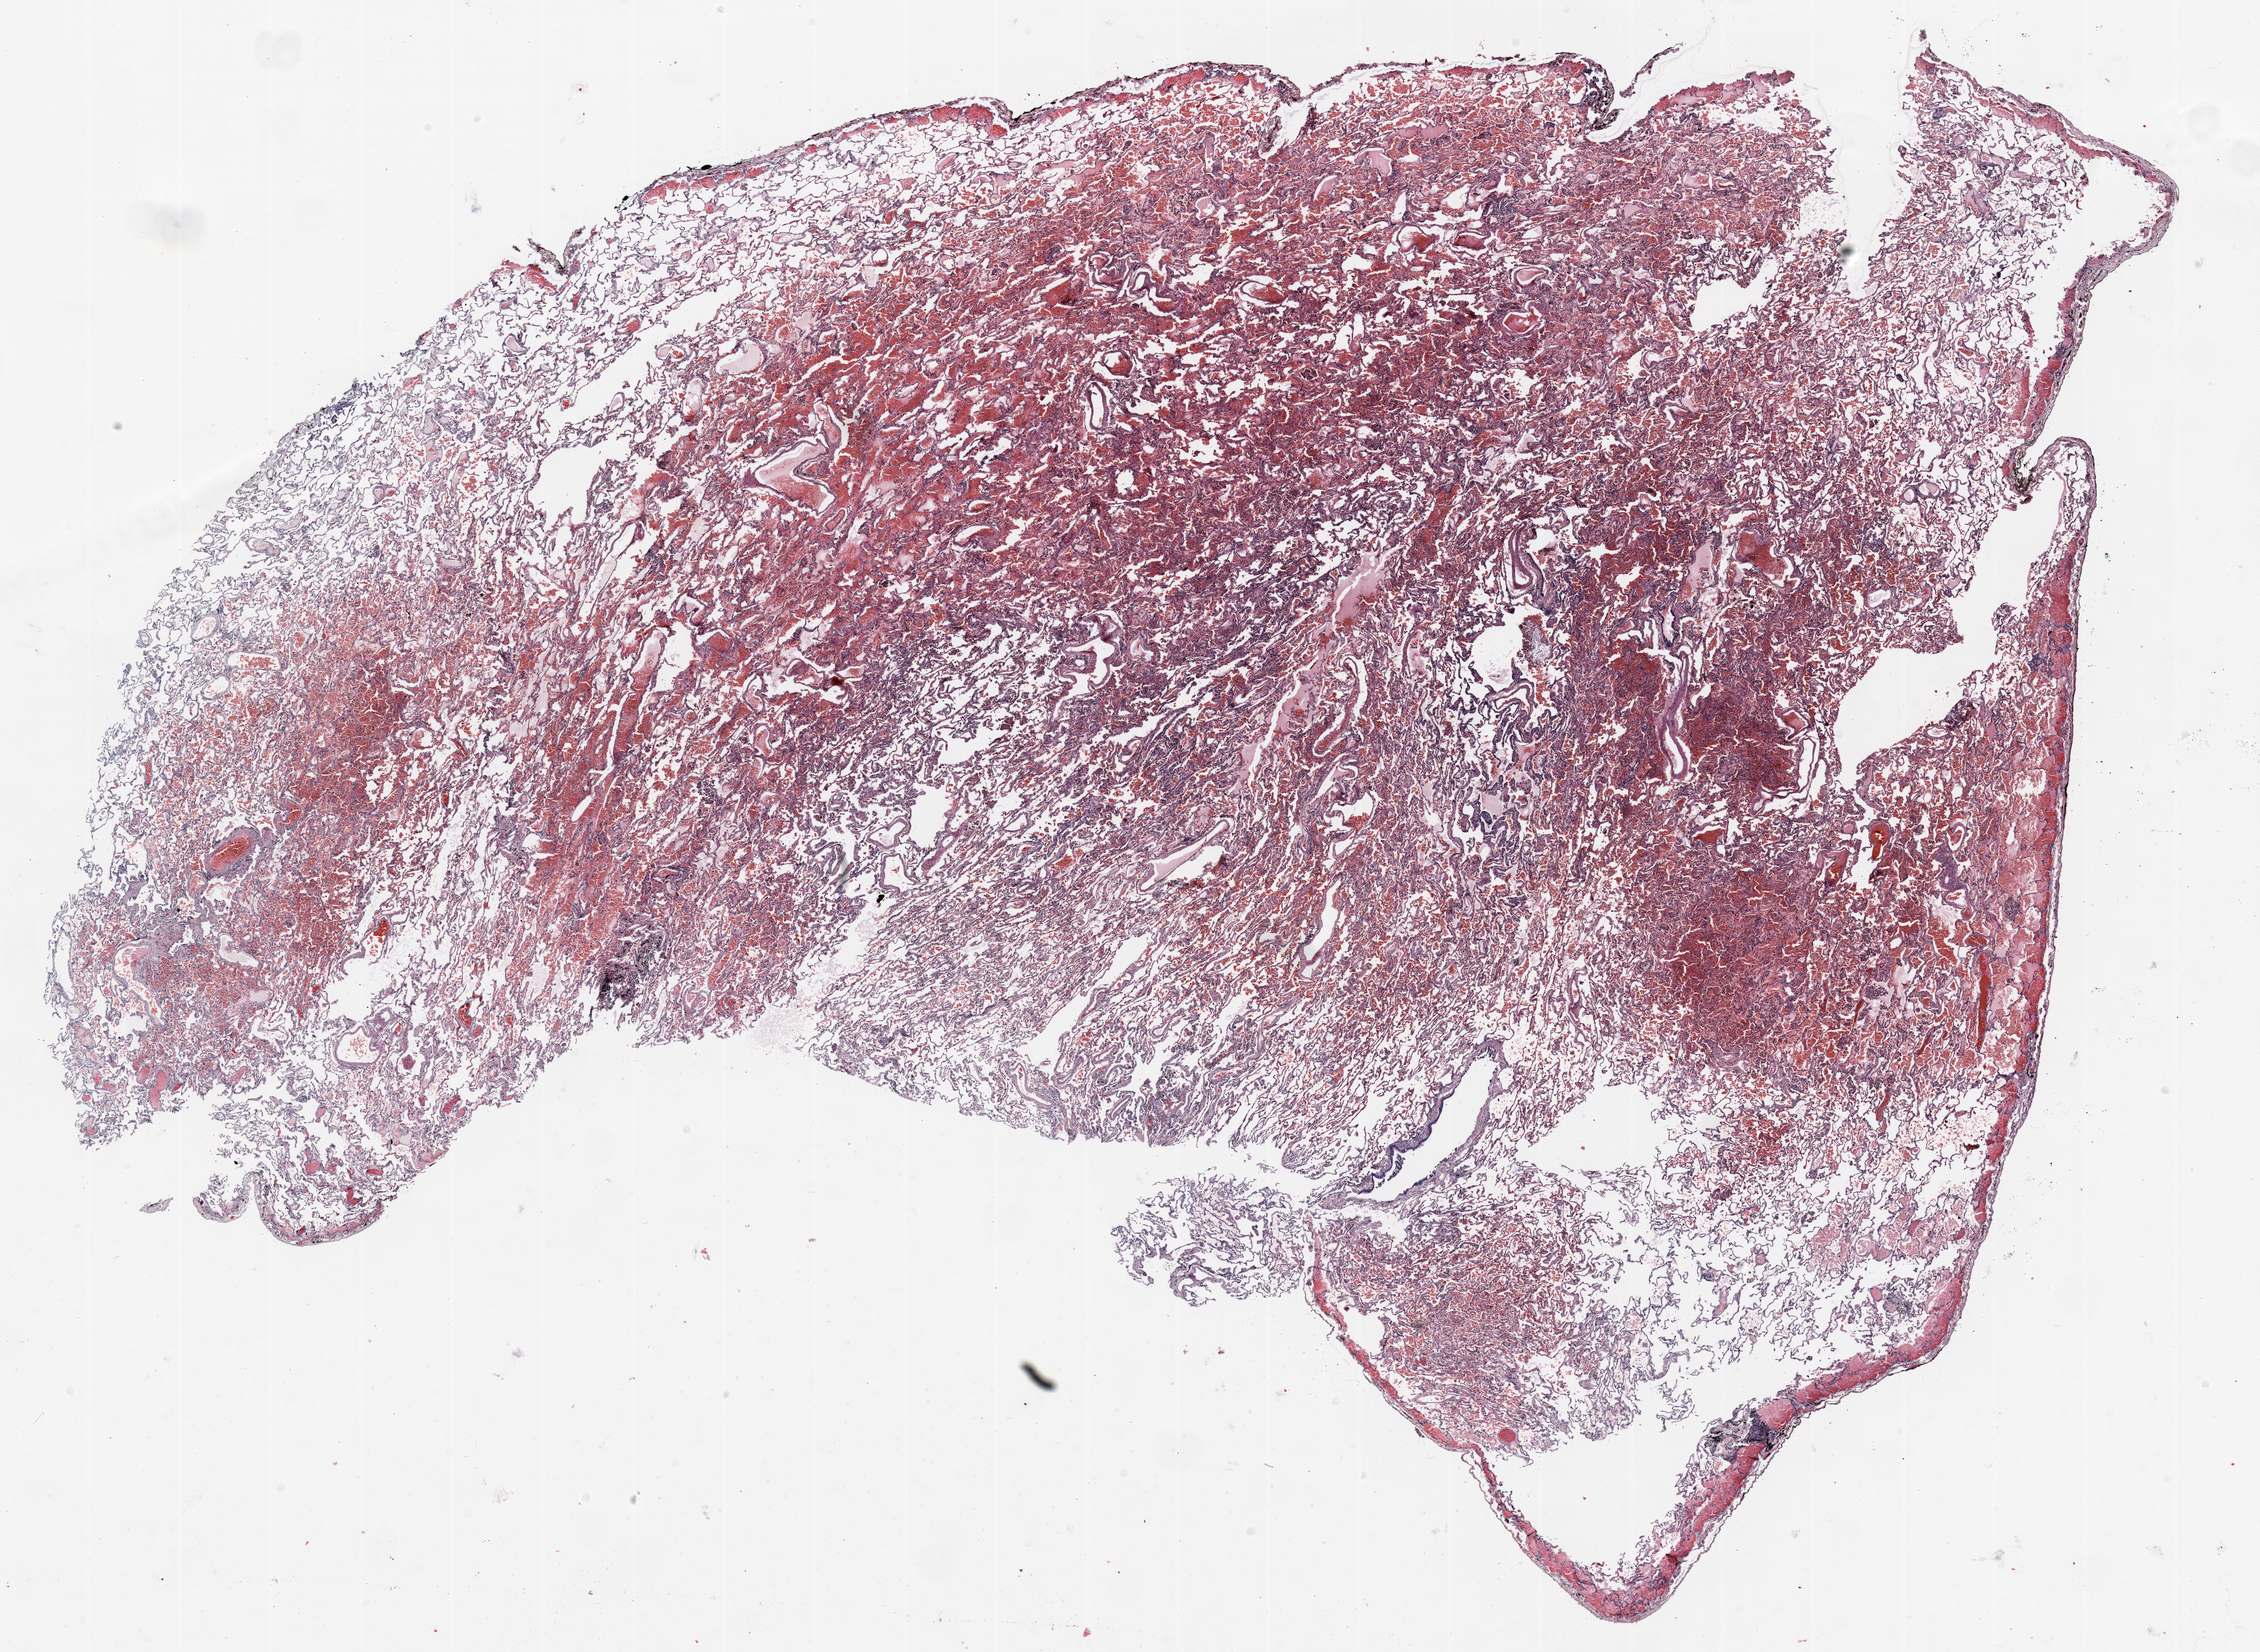
Whole-slide histology image, H&E — shown as a low-resolution overview of the whole scanned area (about 25.0 x 18.3 mm, from a 20x scan), formalin-fixed paraffin-embedded (FFPE) section, lung tissue. Male, age 70 at enrolment. Current smoker at enrolment.
Participant's lung-cancer diagnosis: Adenocarcinoma, NOS.